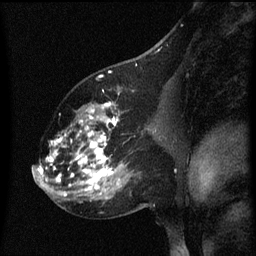
Breast MRI (dynamic contrast-enhanced), one sagittal slice. Slice 33 of 60 in the series (ordered by position). Dynamic contrast-enhanced series, image 2 of 3 at this slice position (ordered by acquisition). 1.5 T. TE 4.2 ms, TR 8 ms. 256 × 256 image matrix, field of view 200 × 200 mm. Patient: female, 60 years.
Annotated regions visible in this slice (semi-automatically segmented with operator editing):
- analysis volume of interest (the breast-tissue region the enhancement analysis was run in; not a lesion): bounding box [x1, y1, x2, y2] px = [49, 102, 158, 197]
- tumour enhancement mask (voxels above the 70 % enhancement threshold inside the analysis volume of interest): [49, 102, 120, 197]